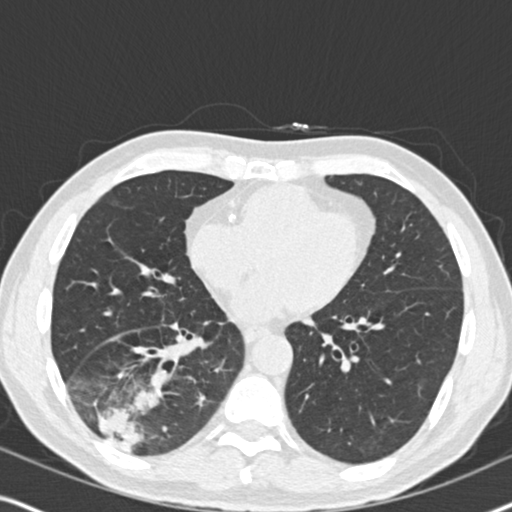
Axial slice from a low-dose chest CT screening exam; second screening round (one year after baseline); lung window (W 1500 / L -600 HU). Male, age 61 years at enrolment. Current smoker at enrolment.
Expert-annotated lung lesion, bounding box <58,338,192,466> (left, top, right, bottom; pixels). The exam's reader record, not a measurement of the box and not confirmed to be the same lesion: non-calcified nodule or mass ≥4 mm, right lower lobe, 90 × 80 mm, soft tissue attenuation, pre-existing on the prior screen: yes; interval growth: yes. Later outcome: lung cancer diagnosed 20 days after this screen — bronchiolo-alveolar adenocarcinoma, NOS, right lower lobe, moderately differentiated (G2), stage IIIB (AJCC 6th edition), 90 mm at pathology.